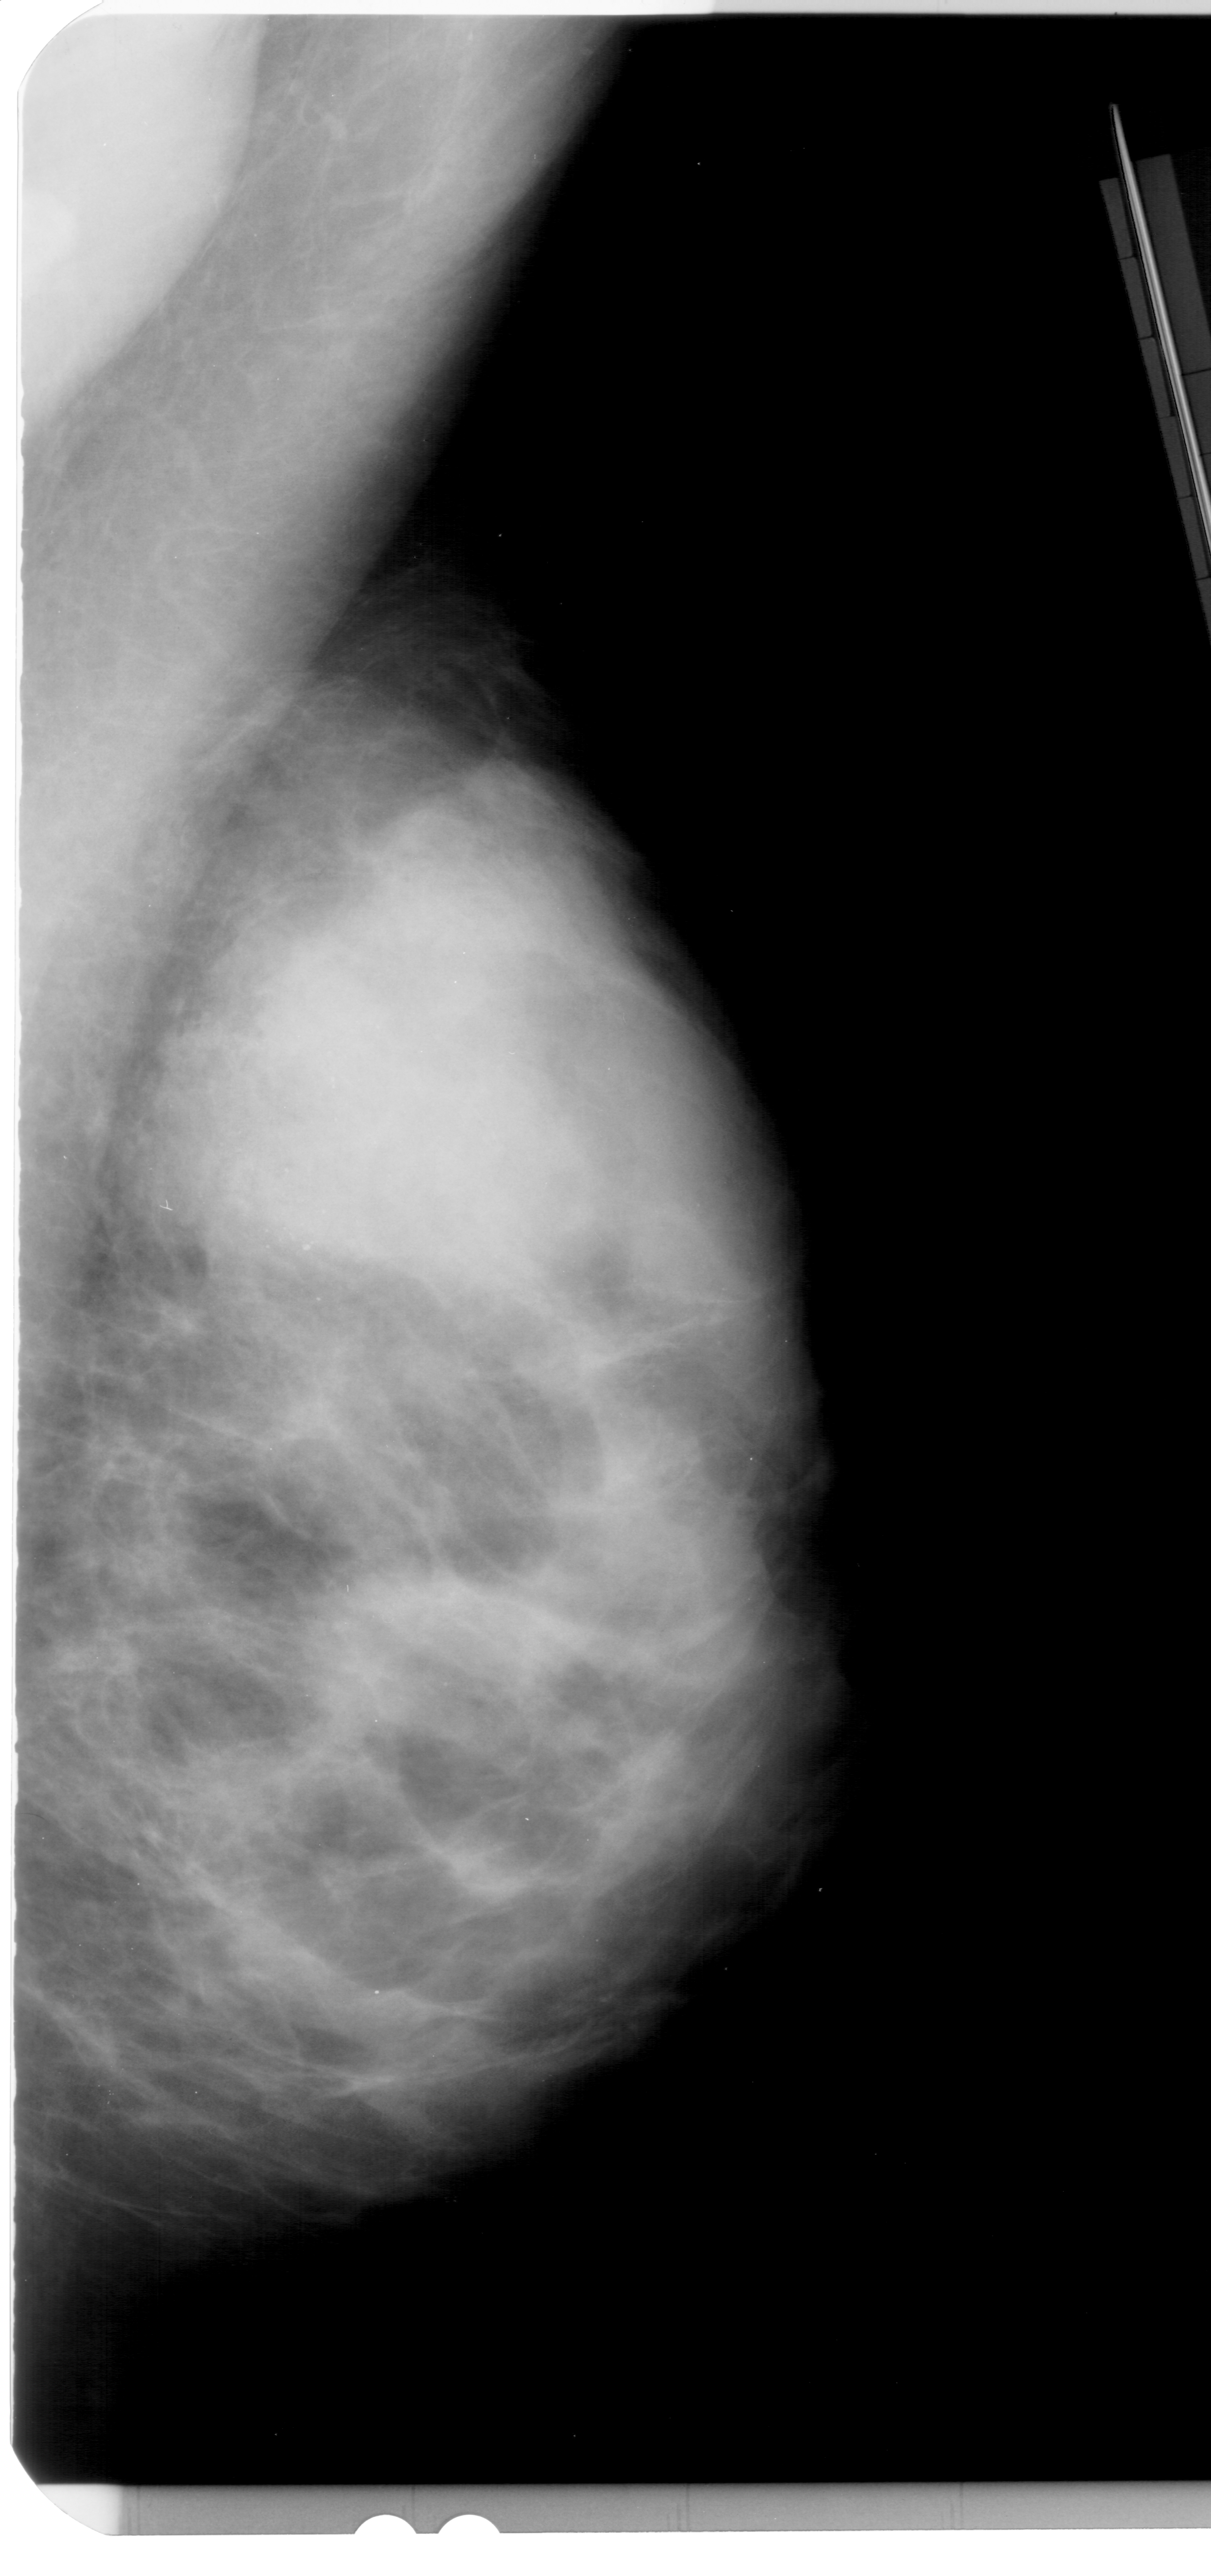
Mammogram (digitized film); right breast; MLO view; breast composition: extremely dense (BI-RADS density category 4 of 4); 1211 × 2576 image matrix.
Expert-marked regions of interest on this image (one box per marked abnormality):
- calcifications, morphology amorphous, distribution segmental; BI-RADS assessment category 4; pathology (as recorded): benign: bounding box <110,910,431,1376> (left, top, right, bottom; pixels)